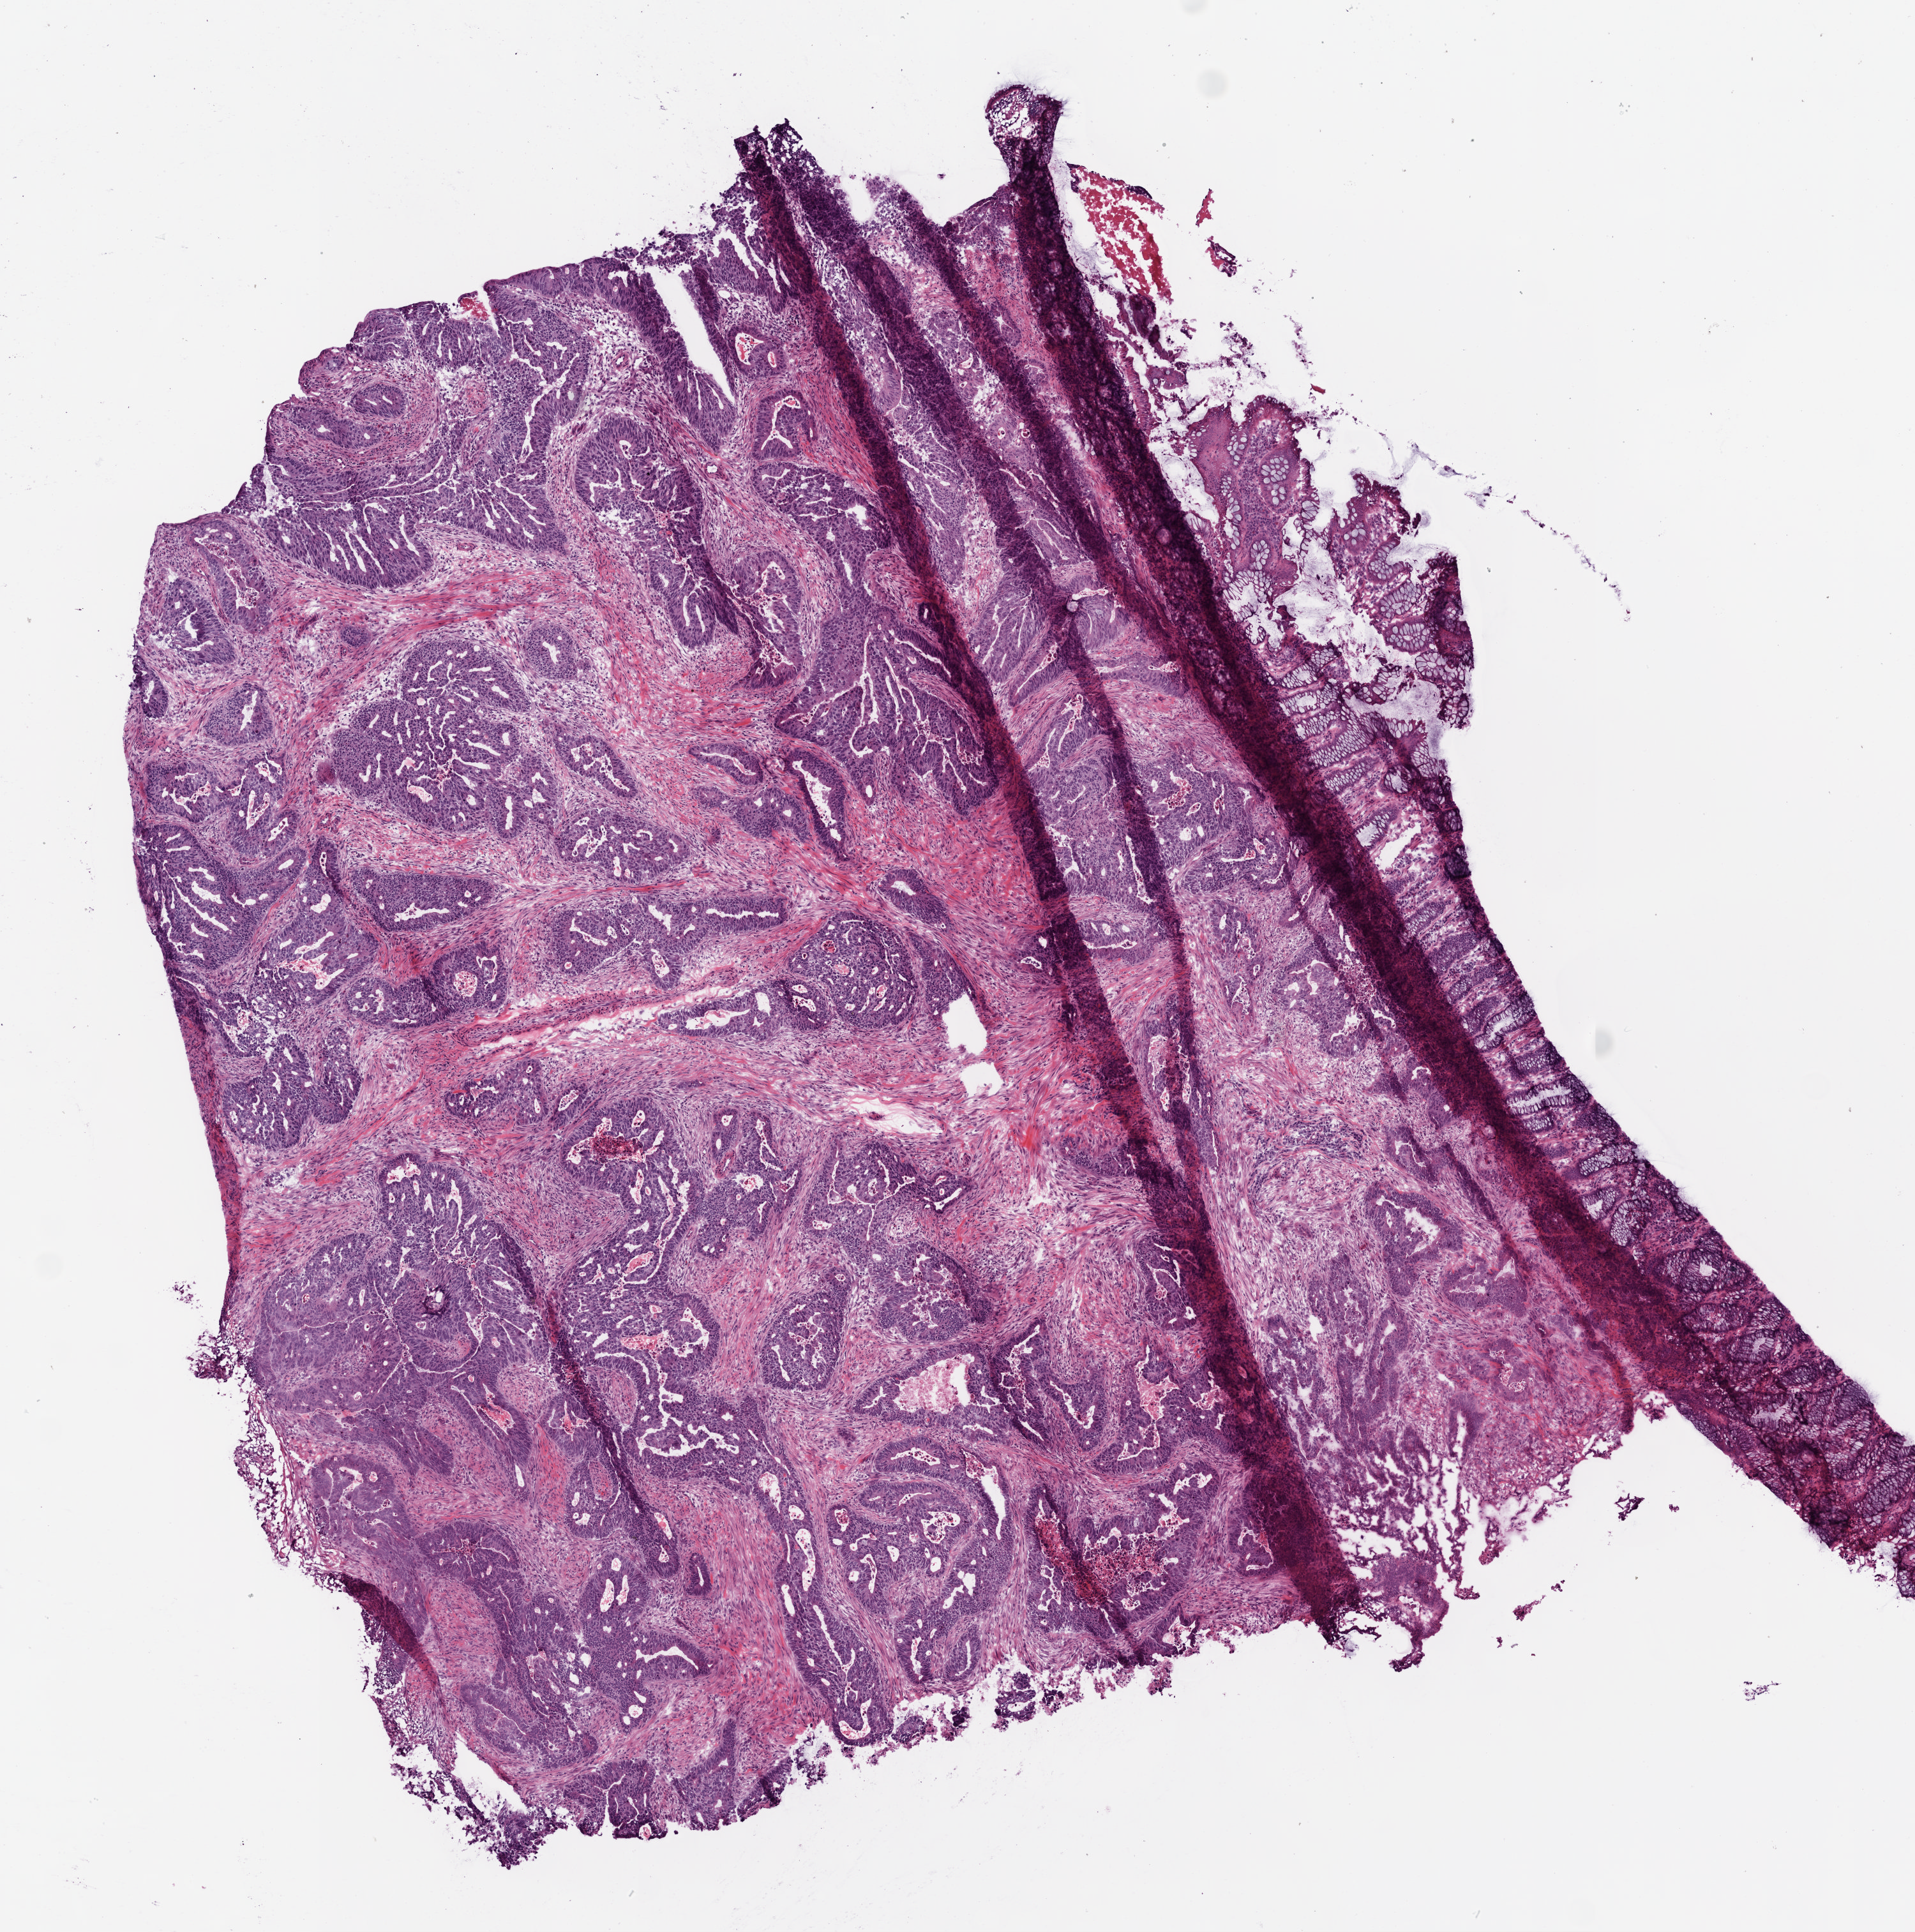
H&E-stained whole-slide image, shown as a low-resolution overview of the whole scanned area (about 6.0 x 6.1 mm, from a 20x scan); frozen section from the bottom of the tissue portion; sample: primary tumour, colon. Female patient; age at initial diagnosis 51 years. Slide review estimates, as recorded: tumour cells 60%, tumour nuclei 80%, normal cells 0%, stromal cells 40%, necrosis 0%.
* AJCC pathologic stage: II (5th edition)
* pathologic diagnosis: Adenocarcinoma, NOS
* lymph nodes positive (case pathology): 0 of 33 examined